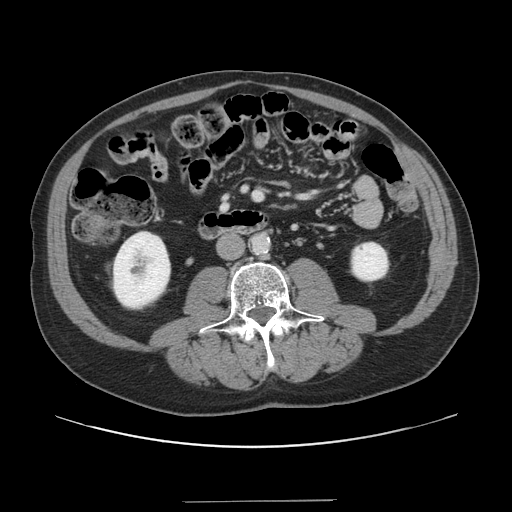
Contrast-enhanced abdominal CT, one axial slice; position 29 of 151 along the scan axis; intravenous contrast given; soft-tissue window (W 400 / L 40 HU); 512 × 512 image matrix, field of view 399 × 399 mm. Male patient, age 63 years. Case-level facts recorded for this patient, not image findings: diagnosis: colorectal cancer liver metastases, imaged before liver resection; multiple liver metastases: no.
Outlined on this slice (outlined manually by an expert reader):
- portal vein (with intrahepatic branches): bounding box <254,192,260,197> (left, top, right, bottom; pixels)